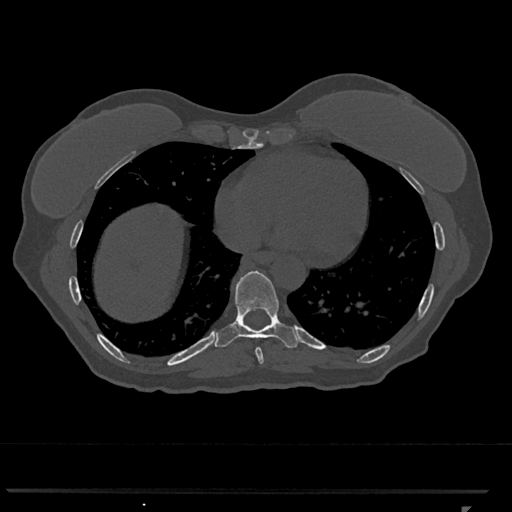
CT including the spine, one axial slice; position 624 of 793 along the scan axis; 120 kVp; bone window (W 1800 / L 400 HU); 512 × 512 image matrix, field of view 380 × 380 mm. Patient: female, 62 years. From the clinical record (not read from this slice): primary cancer: renal.
Annotated regions visible in this slice (semi-automatically segmented with operator editing):
- T8 vertebra: bounding box [x1, y1, x2, y2] px = [255, 347, 264, 364]
- T9 vertebra: [215, 270, 299, 348]